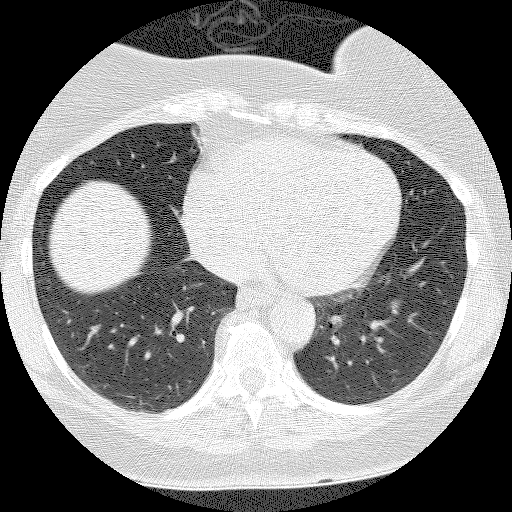
Axial slice from a low-dose chest CT screening exam. First (baseline) screen. Lung window (W 1500 / L -600 HU). Lung (sharp) reconstruction kernel (BONE). Slice 89 of 135 in the series. 512 × 512 image matrix. Female participant, aged 55 years at enrolment. Former smoker at enrolment.
Lesion marked by an expert reader, bounding box <372,285,420,326> (left, top, right, bottom; pixels). The screening reader recorded 3 non-calcified nodules or masses ≥4 mm on this exam (left lower lobe, right lower lobe, right lower lobe); which of them this box marks is not recorded. Official screen result: positive, change unspecified: nodule(s) >= 4 mm or enlarging nodule(s), mass(es), or other non-specific abnormalities suspicious for lung cancer. Later outcome: lung cancer diagnosed 1026 days after this screen — carcinoid tumor, NOS, left lower lobe, carcinoid, stage not assessed, 10 mm at pathology.